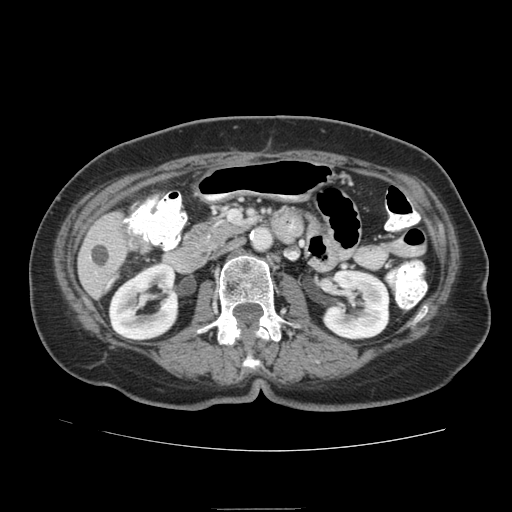
Contrast-enhanced abdominal CT (liver protocol), one axial slice. Slice 26 of 95 in the series (ordered by position). Soft-tissue window (W 400 / L 40 HU). 2.5 mm slice thickness. 512 × 512 image matrix, field of view 360 × 360 mm. Case-level facts recorded for this patient, not image findings: diagnosis: hepatocellular carcinoma (patient treated with transarterial chemoembolisation; whether this scan precedes or follows treatment is not stated here); TNM stage (as recorded): Stage-IVA; Child-Pugh class: B.
Structures marked on this image (semi-automatic segmentation, software-assisted and operator-edited):
- liver parenchyma outside the tumour (the mass and vessels are separate outlines, so this box may not span the whole liver): bounding box (x1, y1, x2, y2) in pixels: (78, 212, 132, 298)